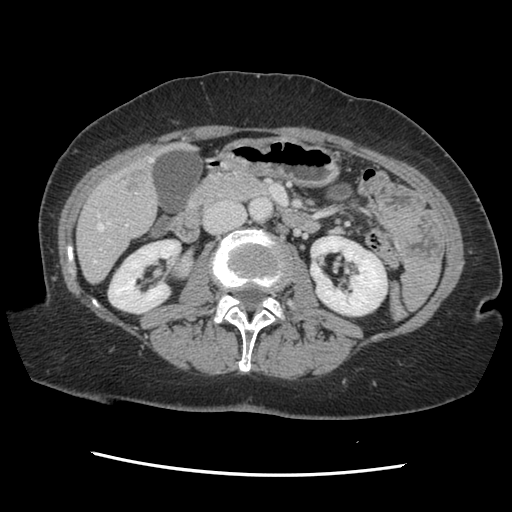
Contrast-enhanced abdominal CT, one axial slice; slice 53 of 141 in the series (ordered by position); soft-tissue window (W 400 / L 40 HU); 2.5 mm slice thickness; 512 × 512 image matrix. Female patient, age 61 years. Case-level facts recorded for this patient, not image findings: diagnosis: colorectal cancer liver metastases, imaged before liver resection; multiple liver metastases: no; largest metastasis: 2.4 cm; disease in both lobes: no.
Structures marked on this image (manually delineated by an expert):
- hepatic veins: box from (x=94, y=158) to (x=153, y=264) px
- liver: (x=78, y=144)–(x=188, y=282)
- planned liver remnant (the part of the liver to remain after resection): (x=78, y=193)–(x=158, y=282)
- portal vein (with intrahepatic branches): (x=100, y=224)–(x=128, y=249)
- liver metastasis: (x=122, y=161)–(x=151, y=194)